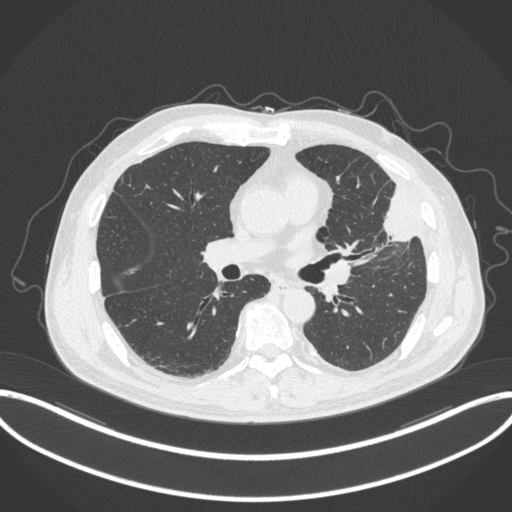
Chest CT, one axial slice; position 179 of 382 along the scan axis; reconstruction kernel B31f; 120 kVp; lung window (W 1500 / L -600 HU); 1 mm slice thickness; 512 × 512 image matrix, field of view 415 × 415 mm. Male patient, age 64 years. Case-level facts recorded for this patient, not image findings: clinical TNM (as recorded): T4 N1 M0.
Outlined on this slice (rectangle marked by the reading radiologist):
- lung tumour (recorded histology: adenocarcinoma): bounding box <378,185,417,246> (left, top, right, bottom; pixels)